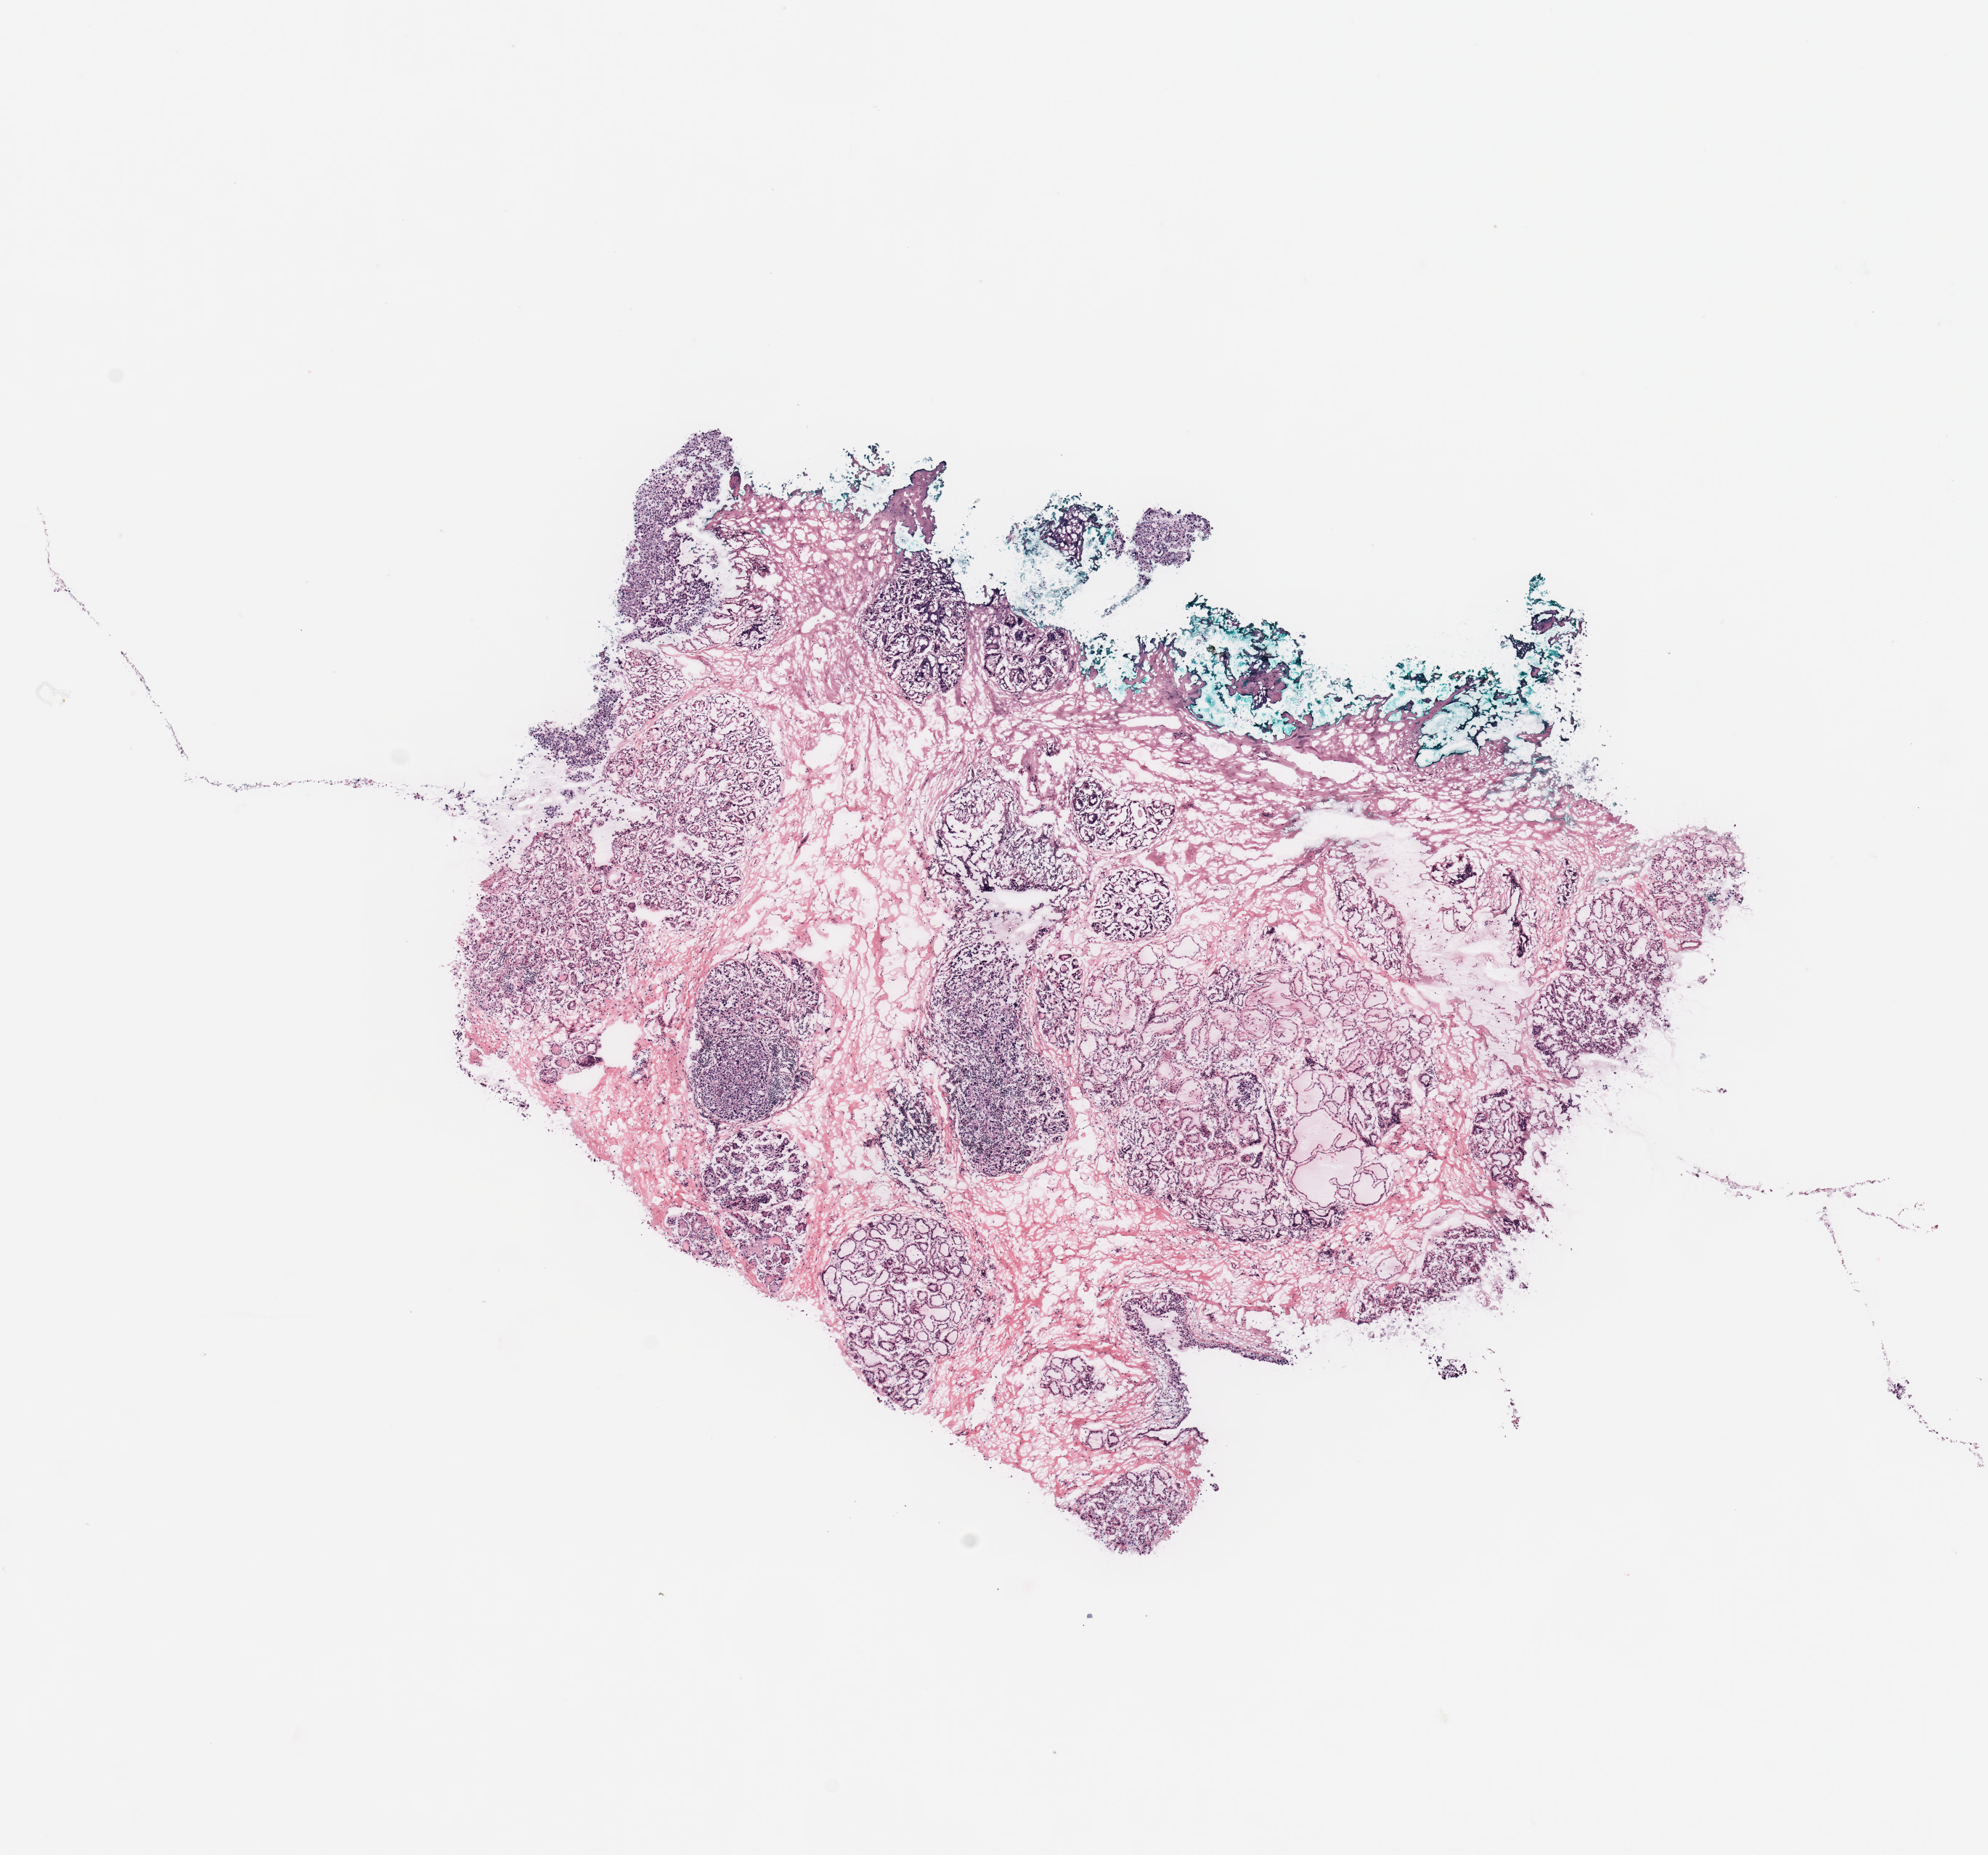
Whole-slide histology image, H&E-stained, whole scanned area (about 10.8 x 10.1 mm, slide scanned at 20x) shown as a low-resolution overview. Breast, tissue type not recorded. 39-year-old female patient.
Patient diagnosis: Infiltrating duct carcinoma, NOS.